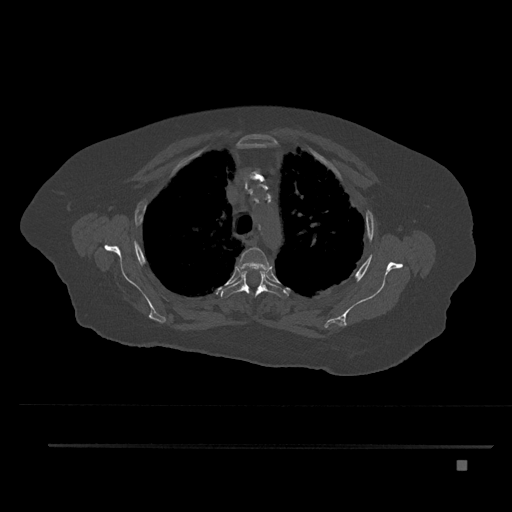
CT including the spine, one axial slice. Position 614 of 797 along the scan axis. Bone window (W 1800 / L 400 HU). 0.5 mm slice thickness. 512 × 512 image matrix, field of view 437 × 437 mm. Female patient, age 76 years. Case-level facts recorded for this patient, not image findings: primary cancer: lung; vertebrae with lytic lesions (as recorded): T11, L3.
Structures marked on this image (semi-automatic segmentation, software-assisted and operator-edited):
- T3 vertebra: bounding box <238,247,271,270> (left, top, right, bottom; pixels)
- T4 vertebra: <220,265,289,299>